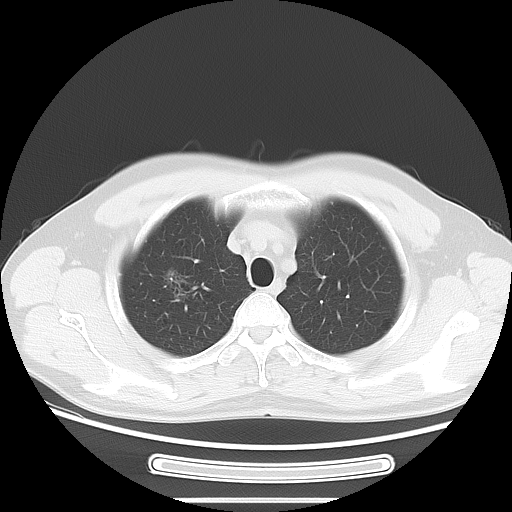
Chest CT, one axial slice; slice 55 of 68 in the series (ordered by position); reconstruction kernel LUNG; 120 kVp; lung window (W 1500 / L -600 HU); 5 mm slice thickness; 512 × 512 image matrix. Male patient, age 53 years. From the clinical record (not read from this slice): clinical TNM (as recorded): T1c N0 M0; histopathological grade: G2.
Structures marked on this image (rectangle marked by the reading radiologist):
- lung tumour (recorded histology: adenocarcinoma): box from (x=159, y=265) to (x=195, y=311) px